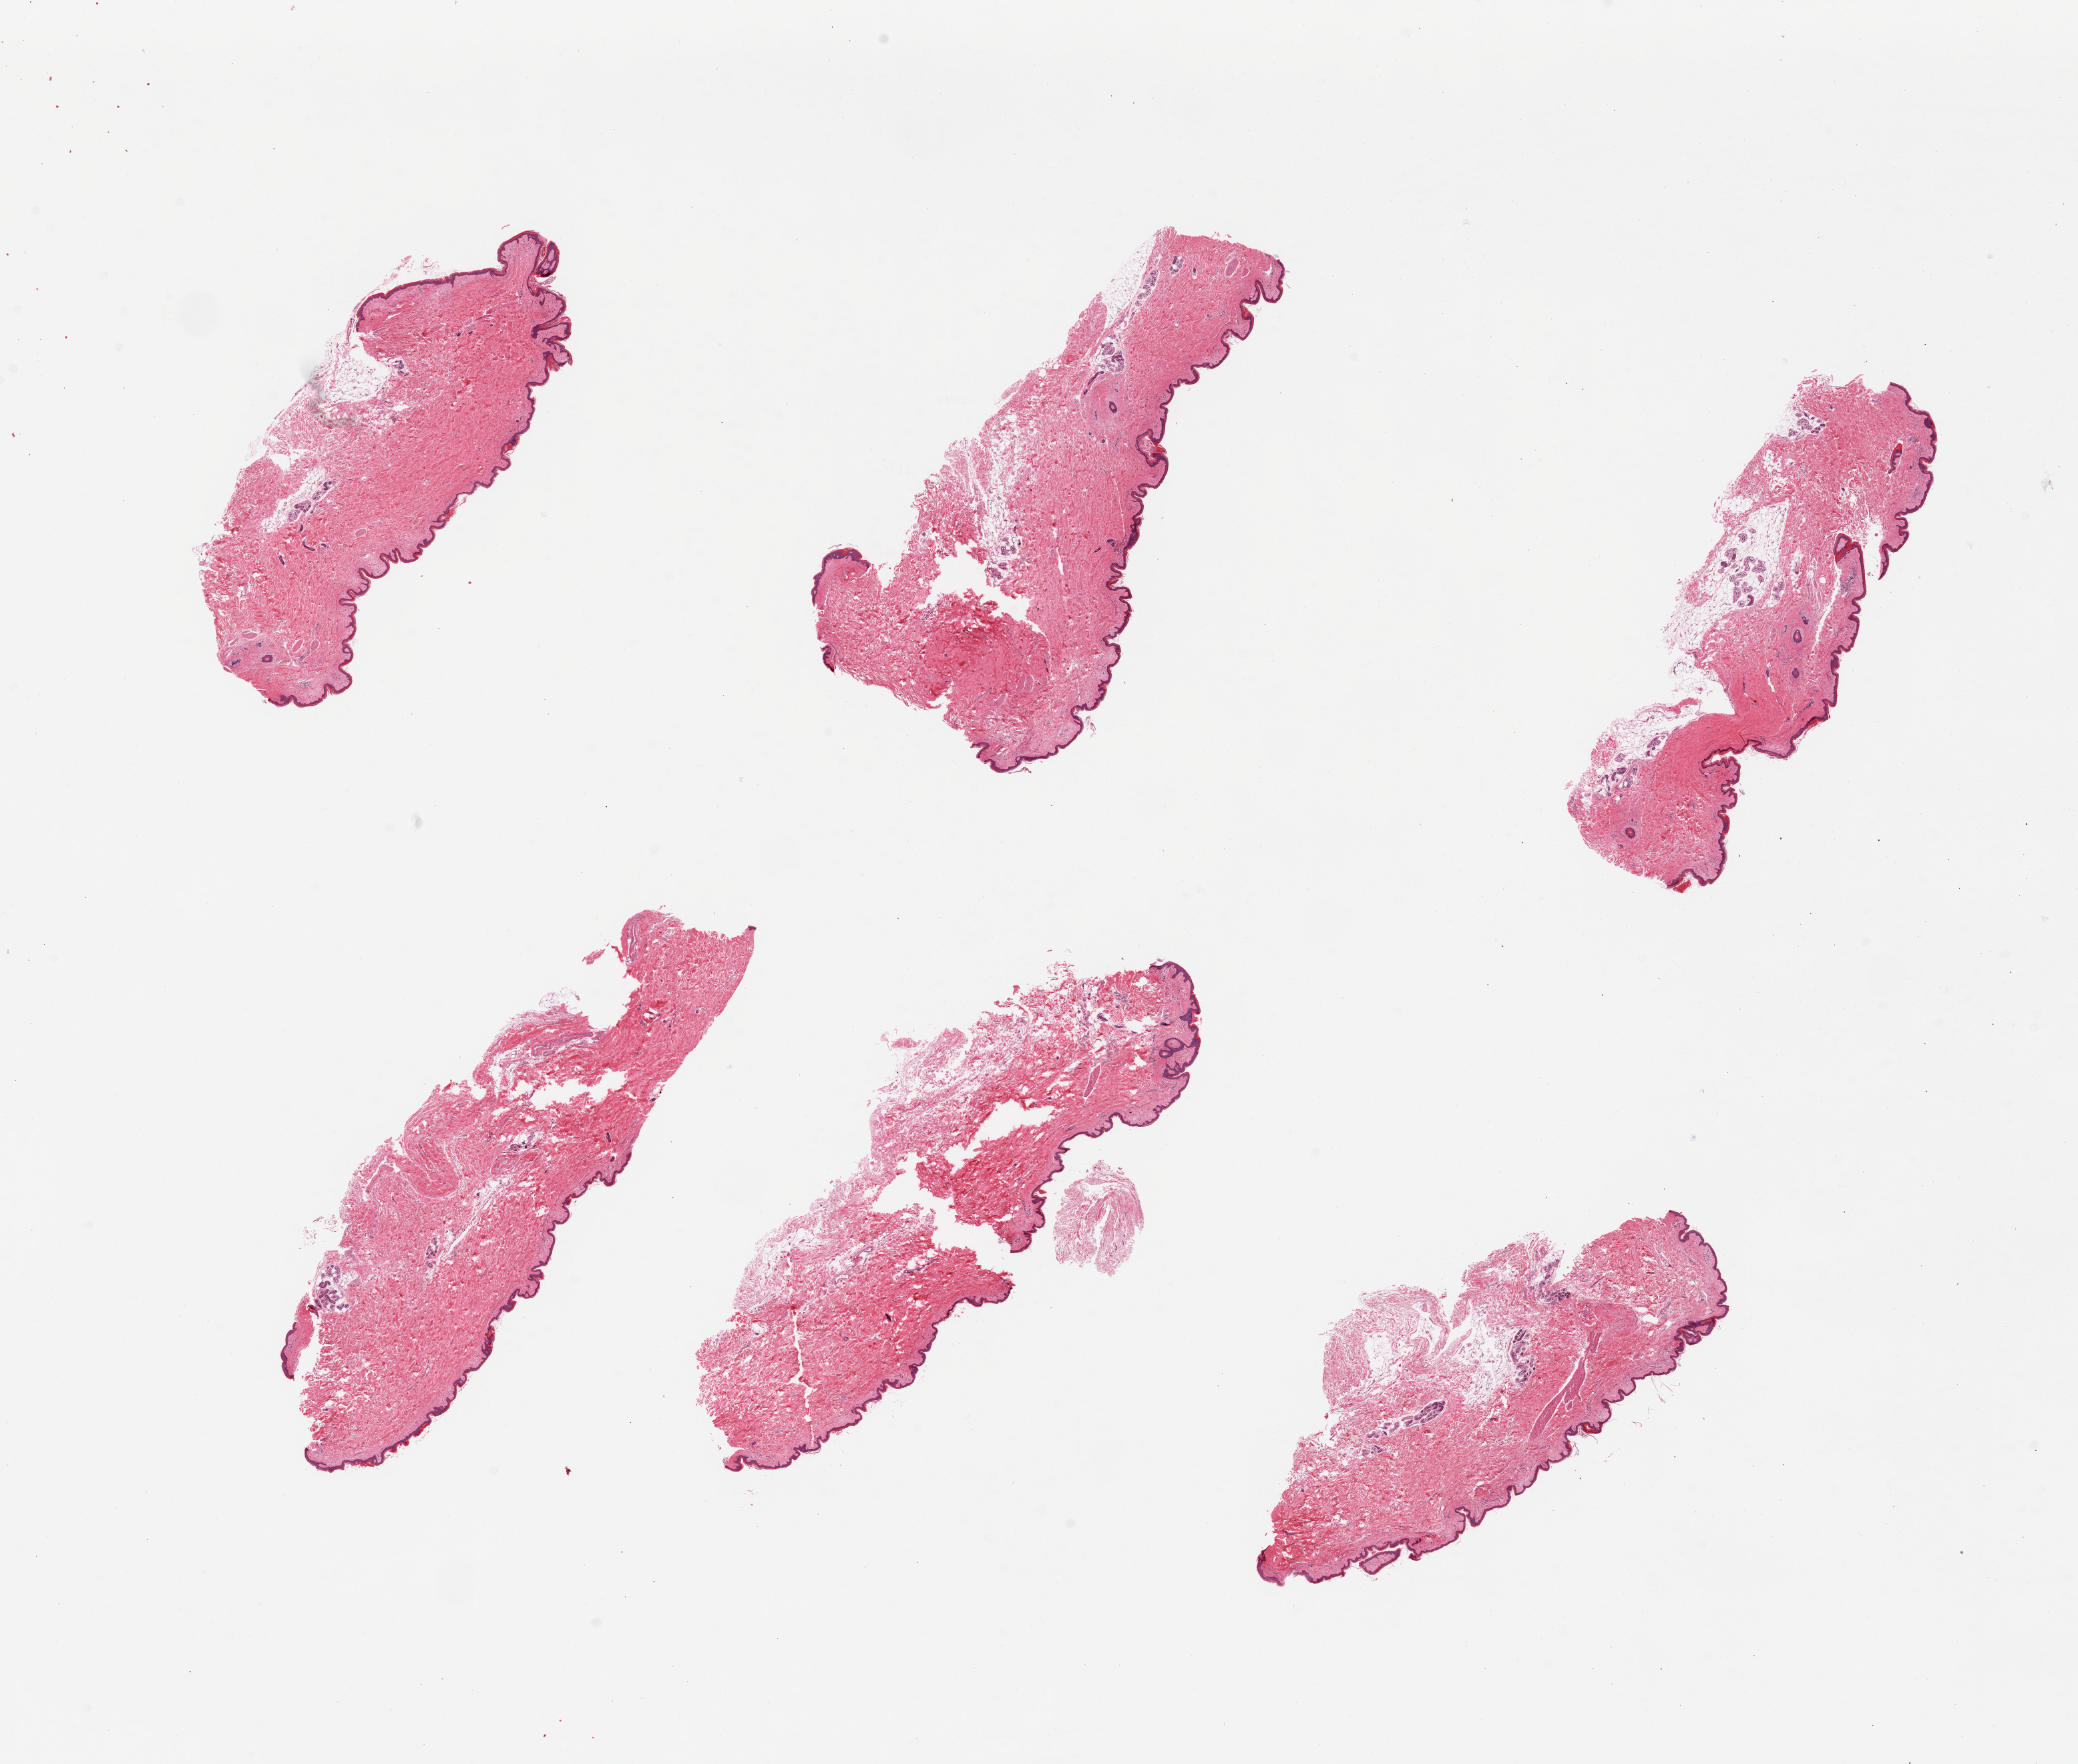
Whole-slide image, H&E stain, brightfield, shown as a low-resolution overview of the whole scanned area (about 24.6 x 20.9 mm, acquisition: 20x scan), PAXgene-fixed, paraffin-embedded tissue, sampled site (target tissue): skin of suprapubic region, donor tissue sample.
• reviewer comment on this tissue sample: 6 pieces; sweat glands moderately autolyzed